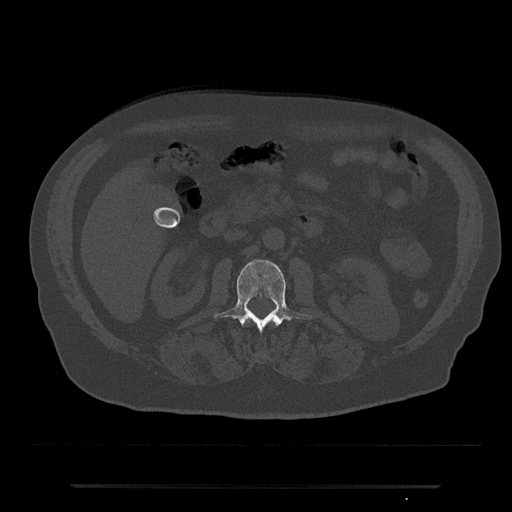
CT including the spine, one axial slice; reconstruction kernel Br40s/3; bone window (W 1800 / L 400 HU); 0.5 mm slice thickness; 512 × 512 image matrix. Patient: male, 80 years. From the clinical record (not read from this slice): primary cancer: prostate; vertebrae with lytic lesions (as recorded): L1, T11.
Annotated regions visible in this slice (semi-automatically segmented with operator editing):
- L1 vertebra: bounding box <244,321,277,325> (left, top, right, bottom; pixels)
- L2 vertebra: <214,259,312,333>